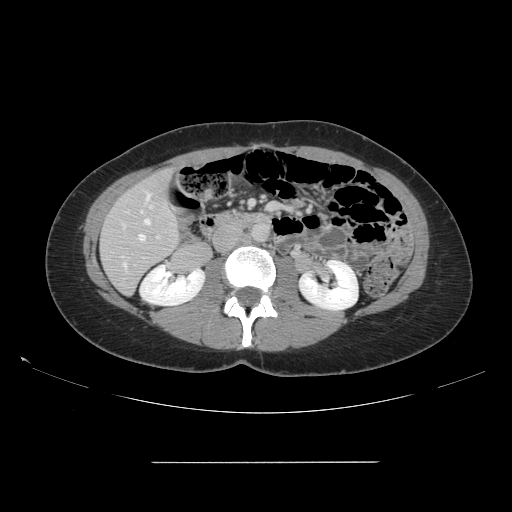
Contrast-enhanced abdominal CT, one axial slice; slice 56 of 151 in the series (ordered by position); 120 kVp; soft-tissue window (W 400 / L 40 HU); 2.5 mm slice thickness; 512 × 512 image matrix, field of view 421 × 421 mm. Female patient, age 46 years. From the clinical record (not read from this slice): diagnosis: colorectal cancer liver metastases, imaged before liver resection; multiple liver metastases: yes; largest metastasis: 3 cm; disease in both lobes: yes.
Outlined on this slice (expert manual segmentation):
- hepatic veins: bounding box (x1, y1, x2, y2) in pixels: (123, 194, 151, 268)
- liver: (101, 170, 179, 294)
- planned liver remnant (the part of the liver to remain after resection): (101, 170, 179, 293)
- portal vein (with intrahepatic branches): (156, 235, 160, 239)